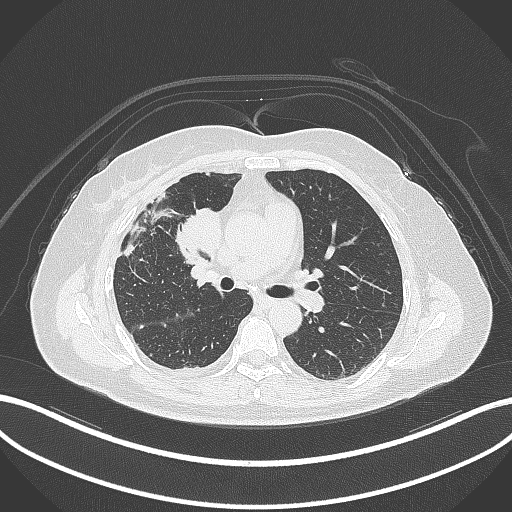
Chest CT, one axial slice. Position 162 of 305 along the scan axis. Reconstruction kernel B70f. Lung window (W 1500 / L -600 HU). 1 mm slice thickness. 512 × 512 image matrix, field of view 400 × 400 mm. Female patient, age 52 years. From the clinical record (not read from this slice): clinical TNM (as recorded): T3 N1 M1.
Annotated regions visible in this slice (bounding box drawn by a radiologist):
- lung tumour (recorded histology: adenocarcinoma): box from (x=176, y=206) to (x=226, y=264) px